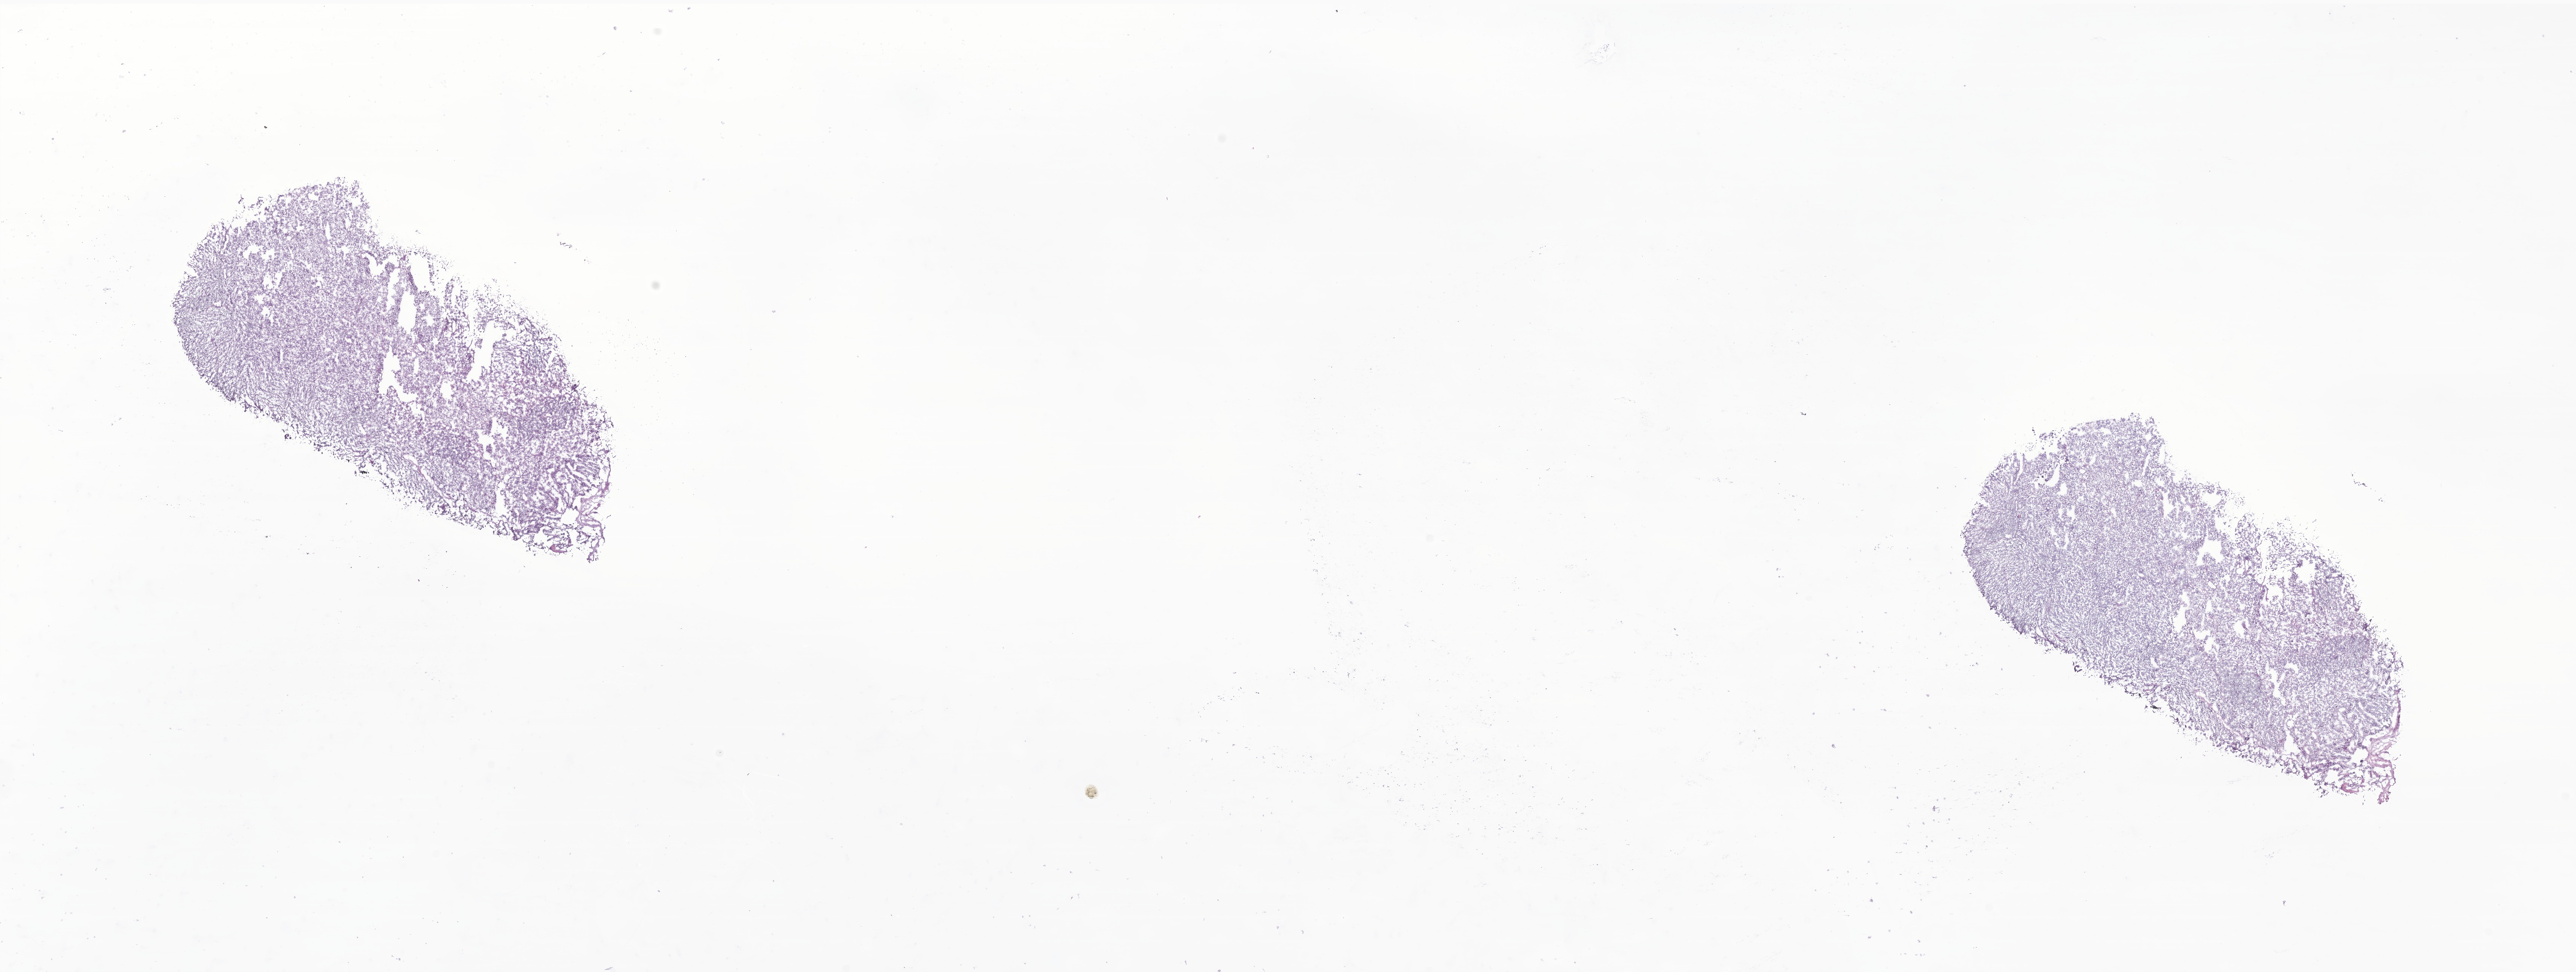
Whole-slide image, haematoxylin and eosin stain of tumor tissue from the retroperitoneum — whole scanned area (about 29.0 x 11.0 mm) shown as a low-resolution overview; frozen section (OCT-embedded). Female patient, age 39 months (3 years 3 months).
Recorded diagnosis: Neuroblastoma, NOS.